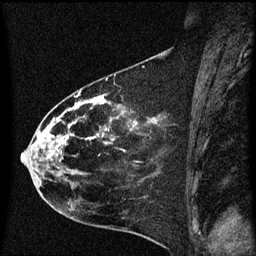
Breast MRI (dynamic contrast-enhanced), one sagittal slice. Position 29 of 60 along the scan axis. Dynamic contrast-enhanced series, image 2 of 3 at this slice position (ordered by acquisition). 1.5 T. TE 4.2 ms, TR 8.4 ms. 2 mm slice thickness. 256 × 256 image matrix, field of view 200 × 200 mm. Patient: female, 35 years. From the clinical record (not read from this slice): setting: breast cancer imaged before/during neoadjuvant chemotherapy; receptor status: HER2-positive.
Outlined on this slice (semi-automatic segmentation, software-assisted and operator-edited):
- analysis volume of interest (the breast-tissue region the enhancement analysis was run in; not a lesion): bounding box [x1, y1, x2, y2] px = [22, 68, 173, 173]
- tumour enhancement mask (voxels above the 70 % enhancement threshold inside the analysis volume of interest): [36, 98, 160, 173]